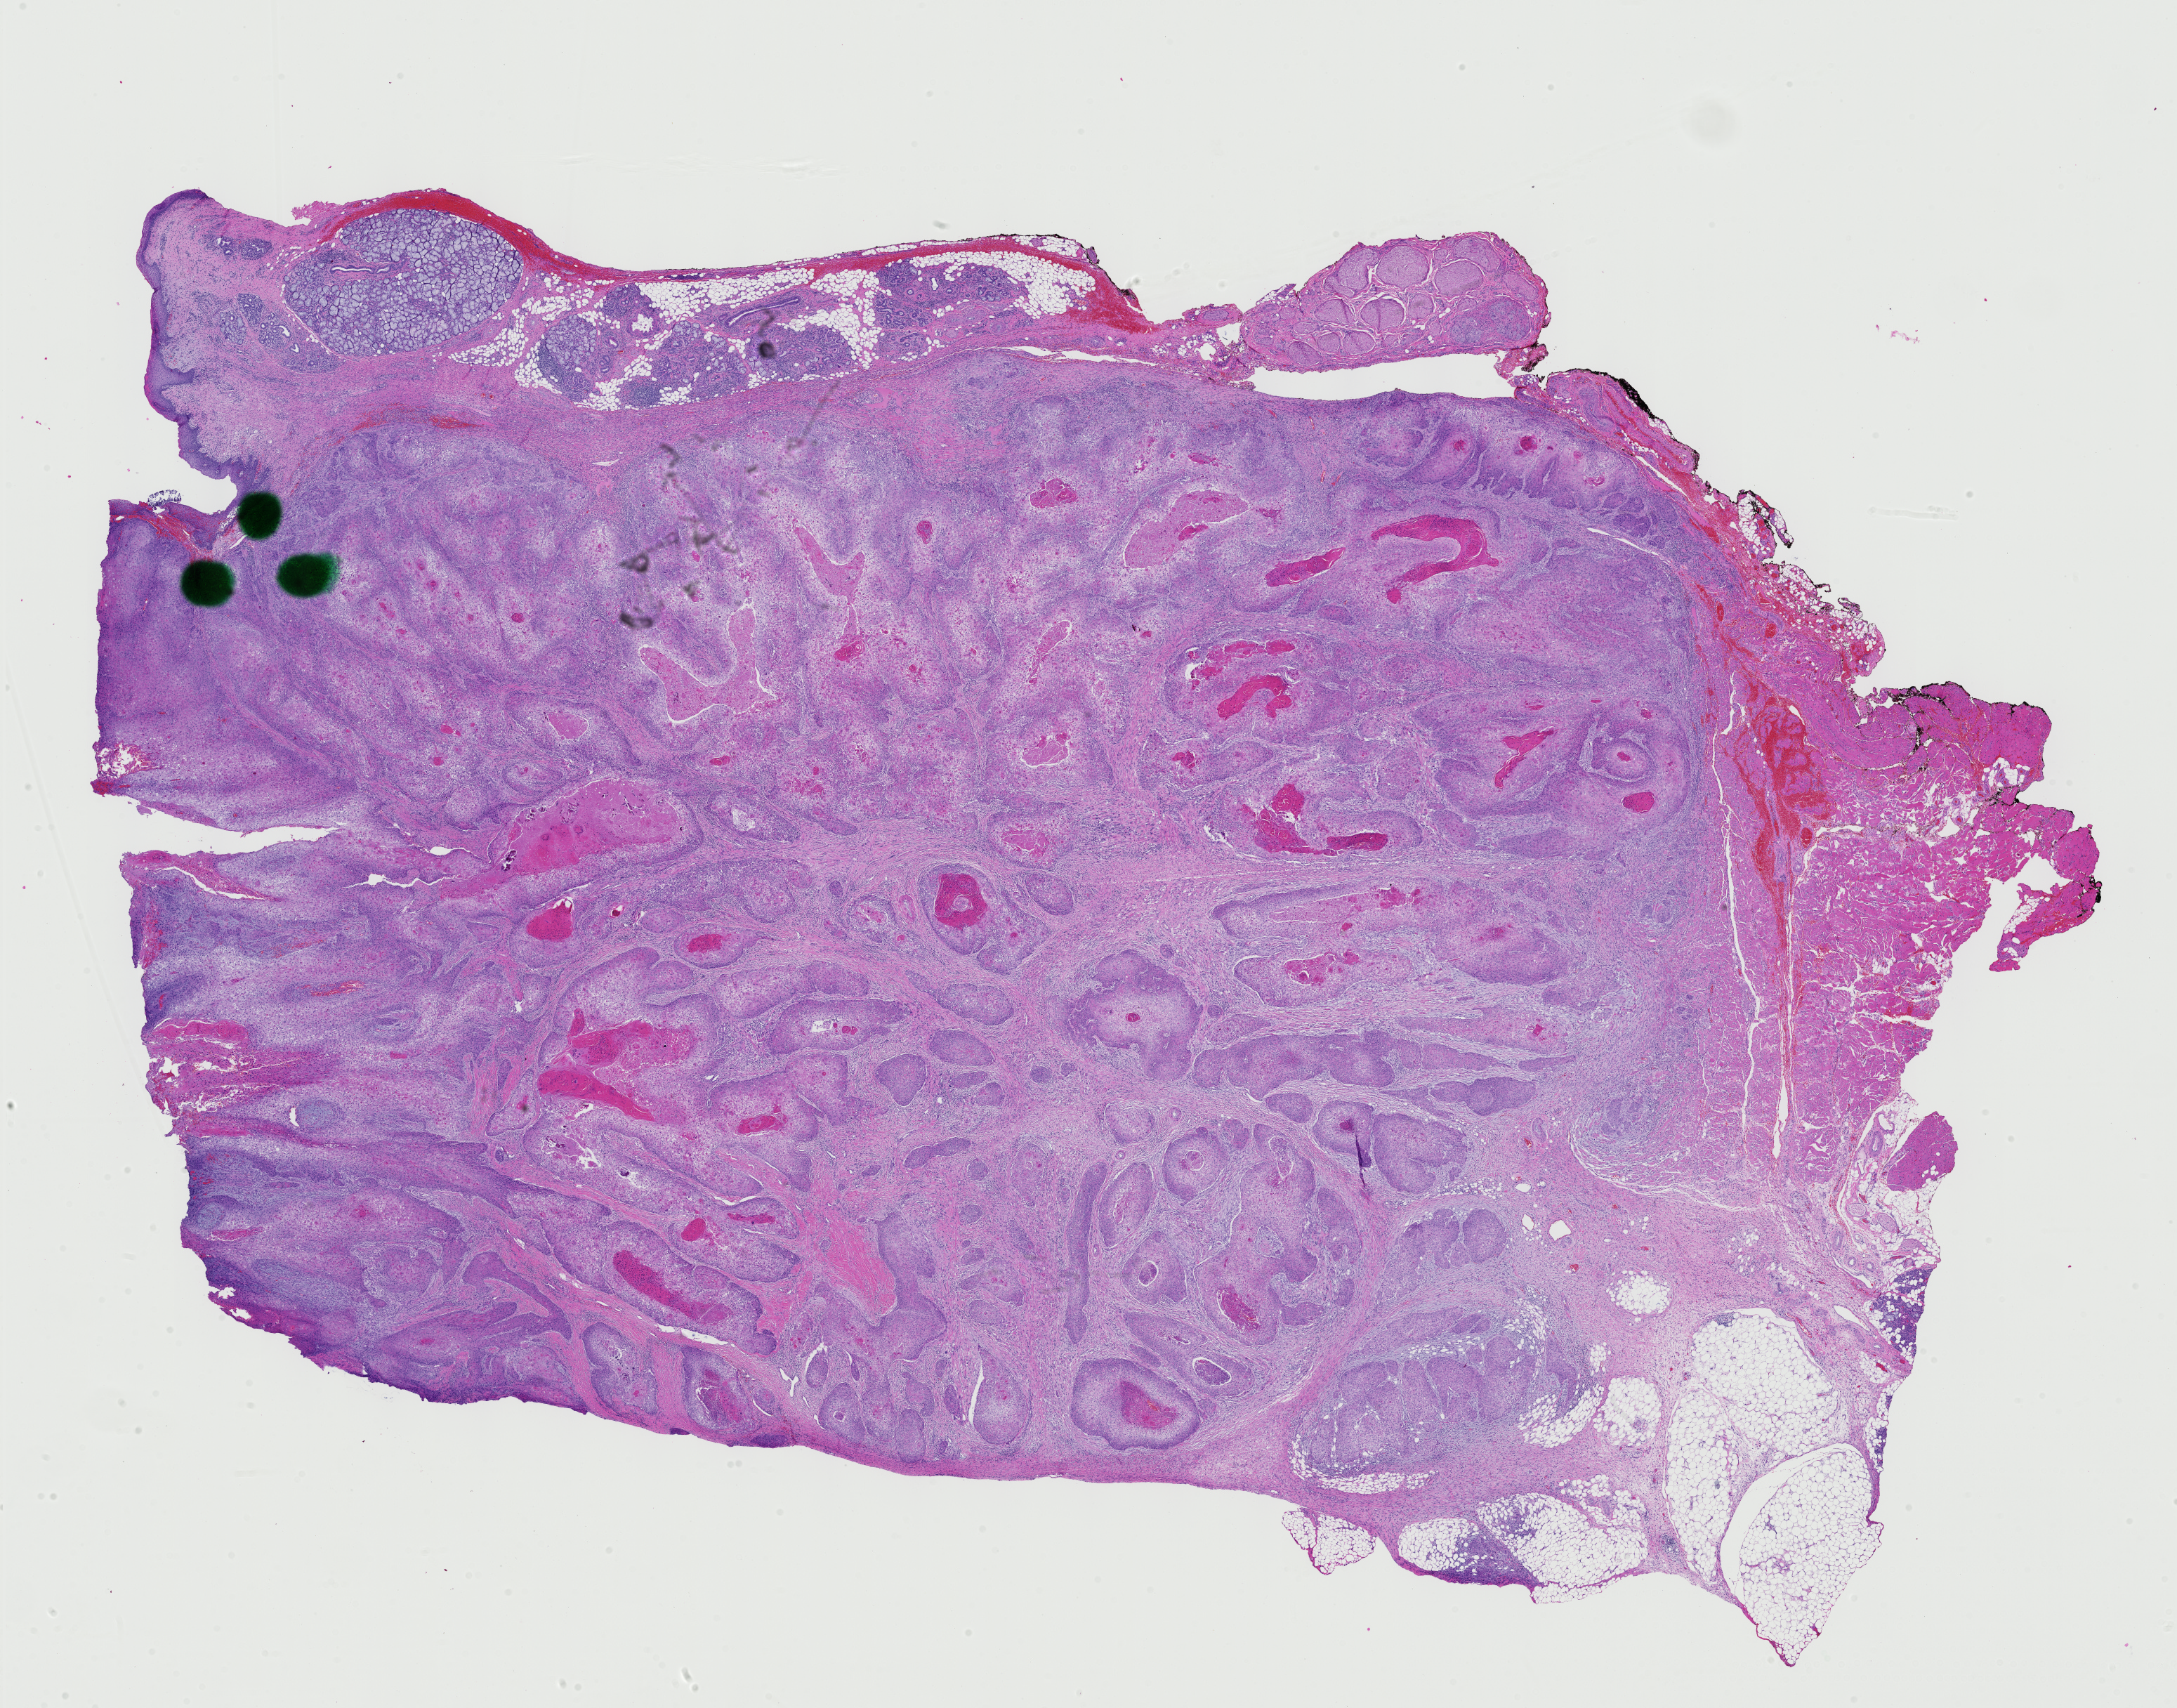
H&E-stained whole-slide image, shown as a low-resolution overview of the whole scanned area (about 22.5 x 17.6 mm, slide scanned at 40x); formalin-fixed paraffin-embedded (FFPE) diagnostic section; primary tumour sample from the head and neck. Female, age 65 years at initial diagnosis. Histologic grade: G2 (moderately differentiated).
* histologic diagnosis: Squamous cell carcinoma, NOS
* laterality: left
* AJCC pathologic stage: IVB